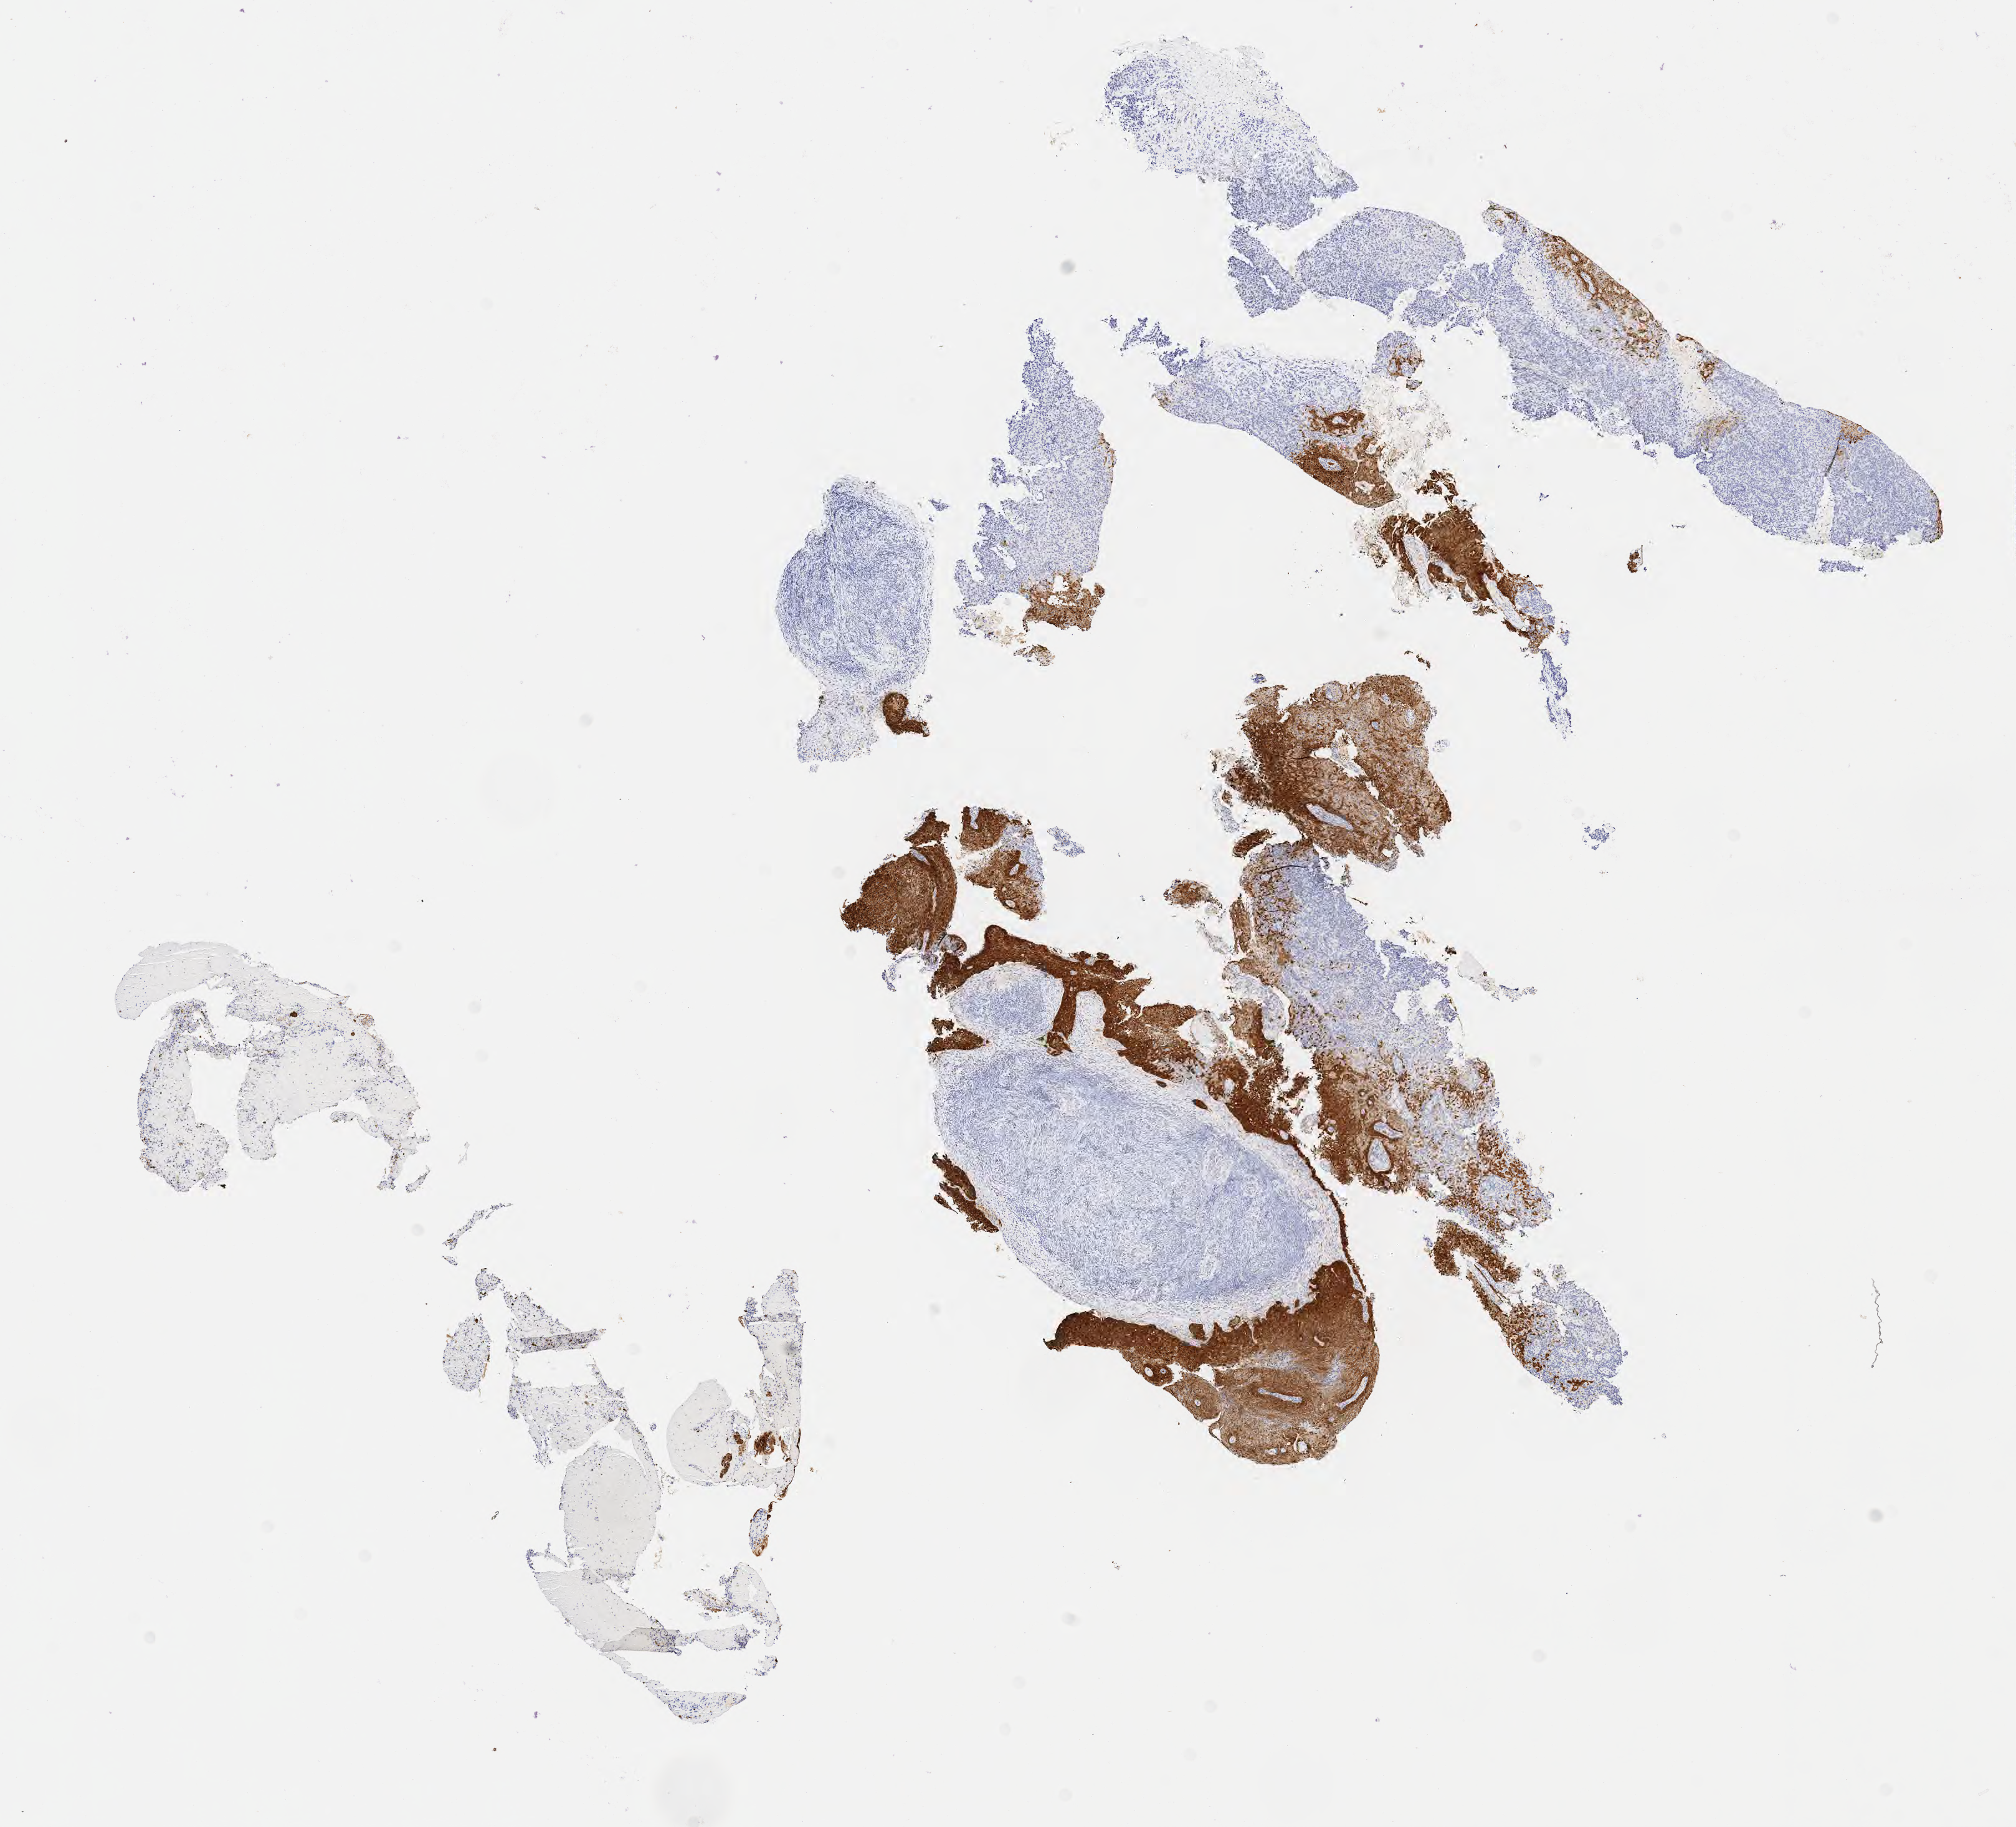
Immunohistochemistry (IHC) whole-slide image stained for p16 (p16INK4a), low-resolution overview of the scanned area, about 13.1 x 11.9 mm; specimen: tumor tissue; site: cervix. Patient female; age 68 years.
Diagnosis: Squamous cell carcinoma, large cell, nonkeratinizing, NOS.